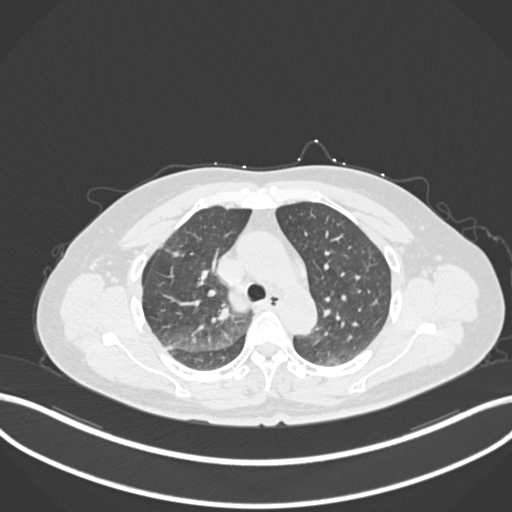
Chest CT, one axial slice. Reconstruction kernel B30f. 120 kVp. Lung window (W 1500 / L -600 HU). 1 mm slice thickness. 512 × 512 image matrix, field of view 400 × 400 mm. Patient: female, 56 years. From the clinical record (not read from this slice): clinical TNM (as recorded): T1c N0 M0.
Outlined on this slice (bounding box drawn by a radiologist):
- lung tumour (recorded histology: adenocarcinoma): bounding box <165,244,179,263> (left, top, right, bottom; pixels)